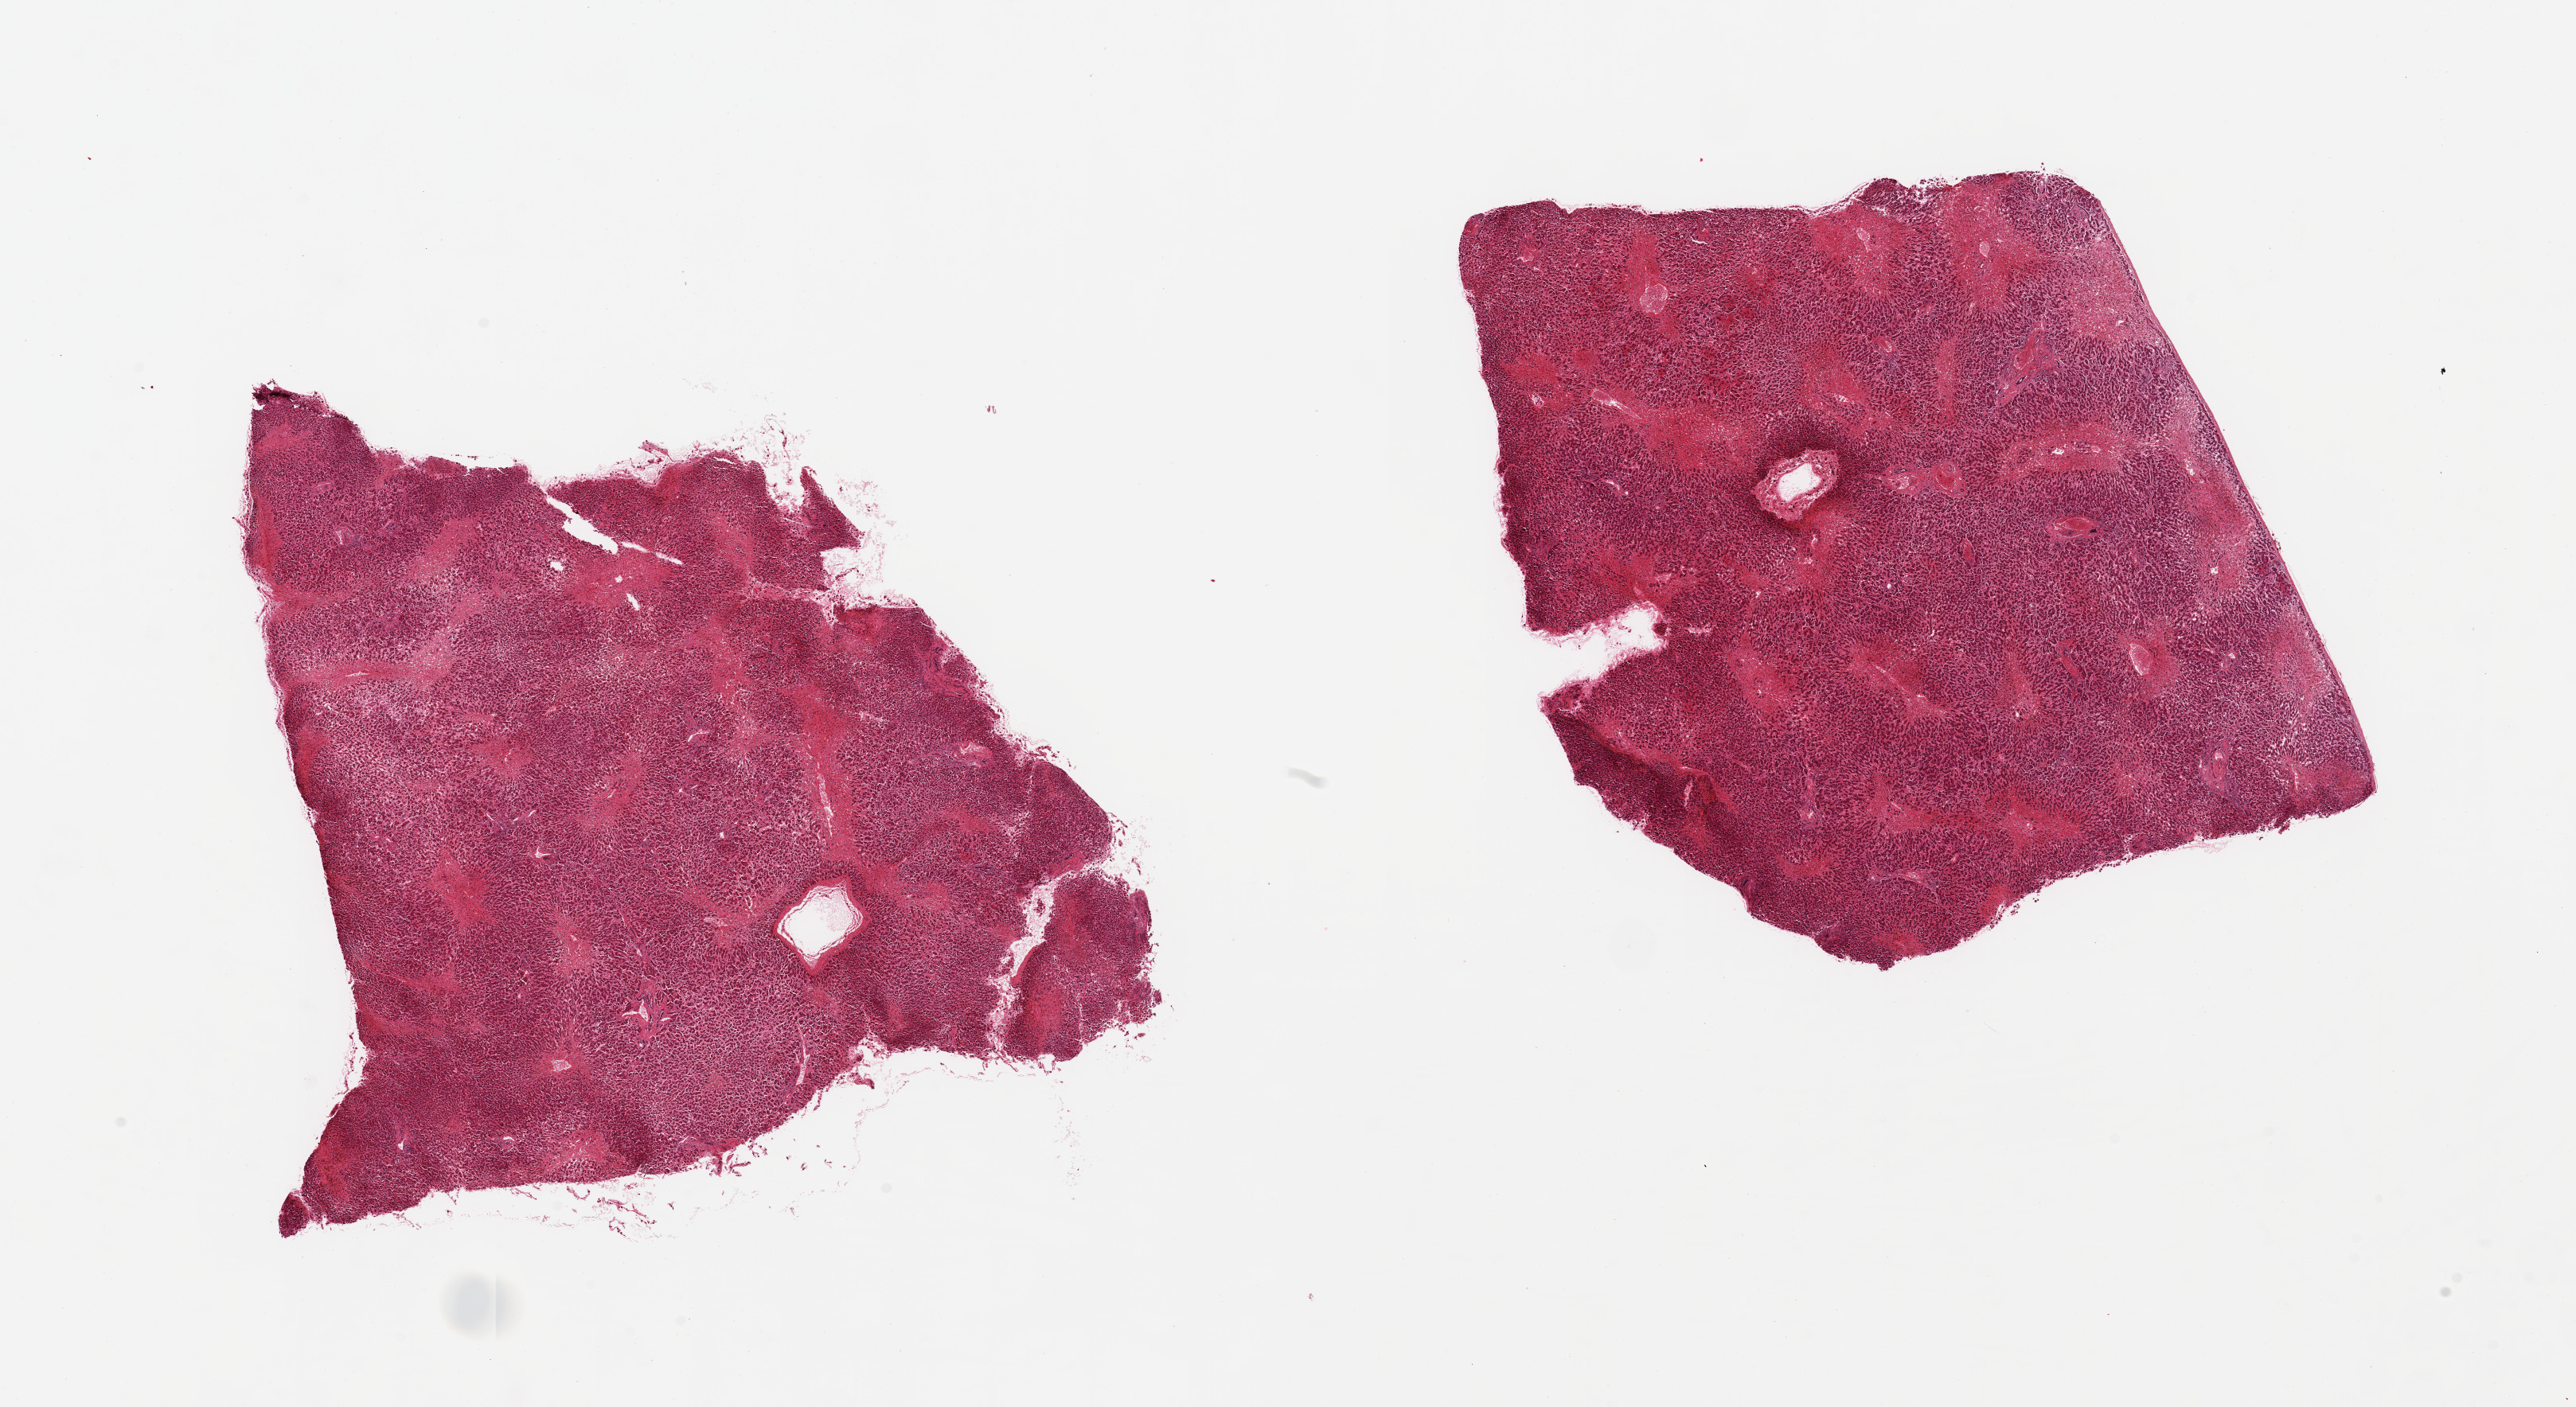
Digitized hematoxylin and eosin (H&E)-stained section, a low-resolution overview of the entire scanned area, about 25.6 x 14.0 mm (acquisition: 20x scan); PAXgene-fixed paraffin-embedded (PFPE) section; sampled site (target tissue): liver; donor tissue sample. Donor: female.
• reviewer comment on this tissue sample: 2 pieces; severe central congestion; no underlying disease